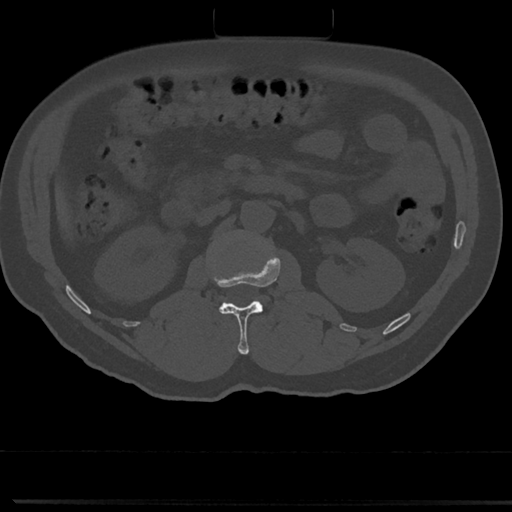
CT including the spine, one axial slice. Reconstruction kernel Br40s/3. 120 kVp. Bone window (W 1800 / L 400 HU). 512 × 512 image matrix, field of view 355 × 355 mm. Patient: male, 61 years. Case-level facts recorded for this patient, not image findings: primary cancer: prostate.
Outlined on this slice (semi-automatically segmented with operator editing):
- L1 vertebra: box from (x=211, y=253) to (x=280, y=354) px